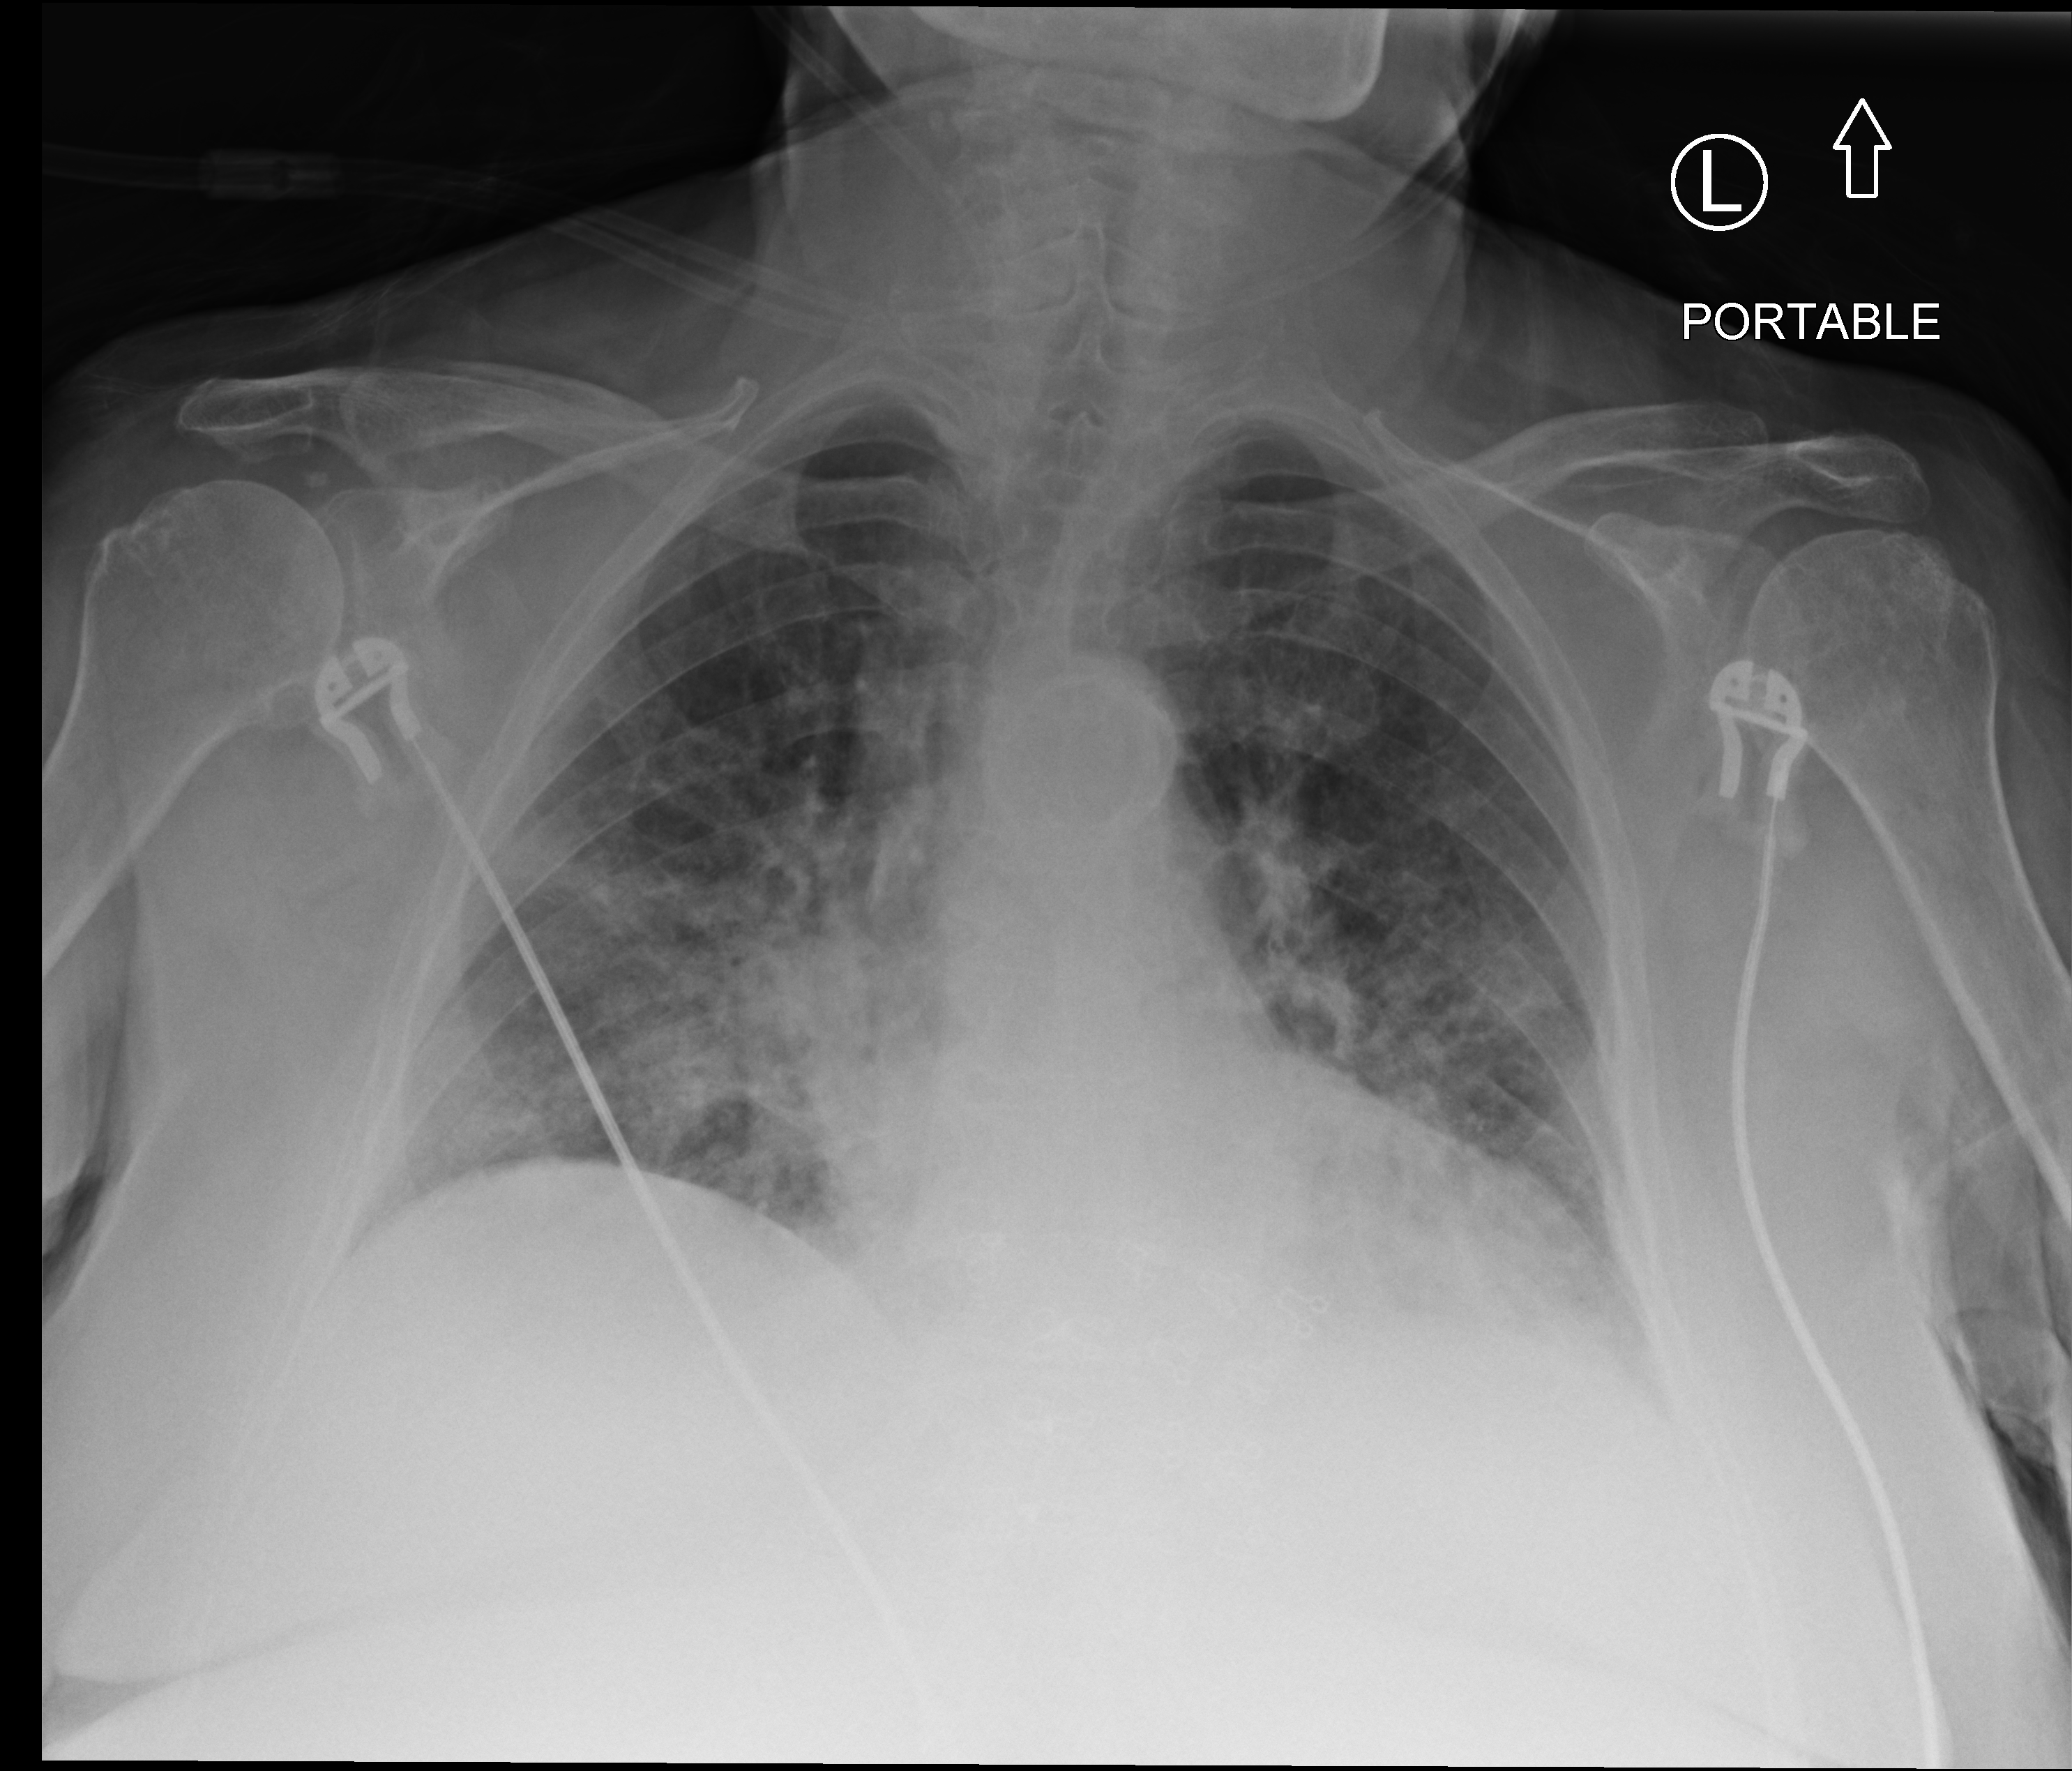
Bedside chest radiograph (computed radiography); anteroposterior (AP) projection. Patient hospitalised with COVID-19; female, aged 75–90 years.
Admission-level facts for this patient (not findings on this image; timing relative to this image not recorded):
- hypertension (admission record): yes
- mechanically ventilated during this hospital stay: no